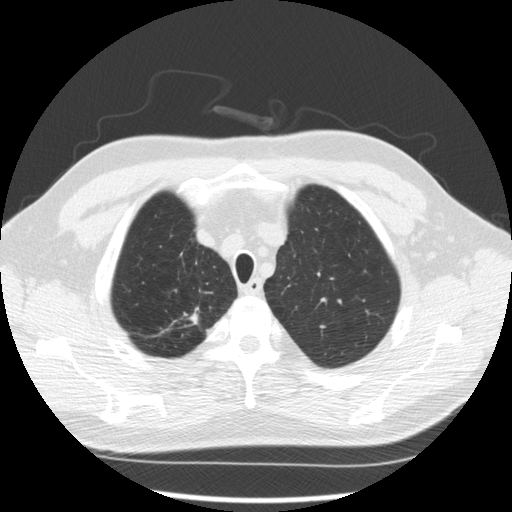
Axial slice from a low-dose chest CT screening exam; second screening round (one year after baseline); lung window (W 1500 / L -600 HU); 2.5 mm slice thickness; standard (soft-tissue) reconstruction kernel (STANDARD); slice 42 of 289 in the series; 512 × 512 image matrix, field of view 360 × 360 mm. Male participant, aged 64 years at enrolment. Former smoker at enrolment.
Expert reader's lesion annotation, bounding box (x1, y1, x2, y2) in pixels: (174, 301, 213, 337). The screening reader recorded 3 non-calcified nodules or masses ≥4 mm on this exam (right upper lobe, right upper lobe, right upper lobe); which of them this box marks is not recorded. Official screen result: positive, other. Lung cancer was diagnosed 411 days after this screen (after the third annual screen): adenocarcinoma, NOS, right upper lobe, moderately differentiated (G2), stage IA (AJCC 6th edition), 14 mm at pathology.